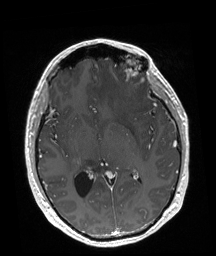
Brain MRI from a brain-tumour surgery series, one axial slice. Position 96 of 192 along the scan axis. T1-weighted post-contrast. 1 mm slice thickness. 216 × 256 image matrix. Case-level facts recorded for this patient, not image findings: tumour location: Left Frontal.
Annotated regions visible in this slice (outlined manually by an expert reader):
- tumour: bounding box <125,59,137,76> (left, top, right, bottom; pixels)